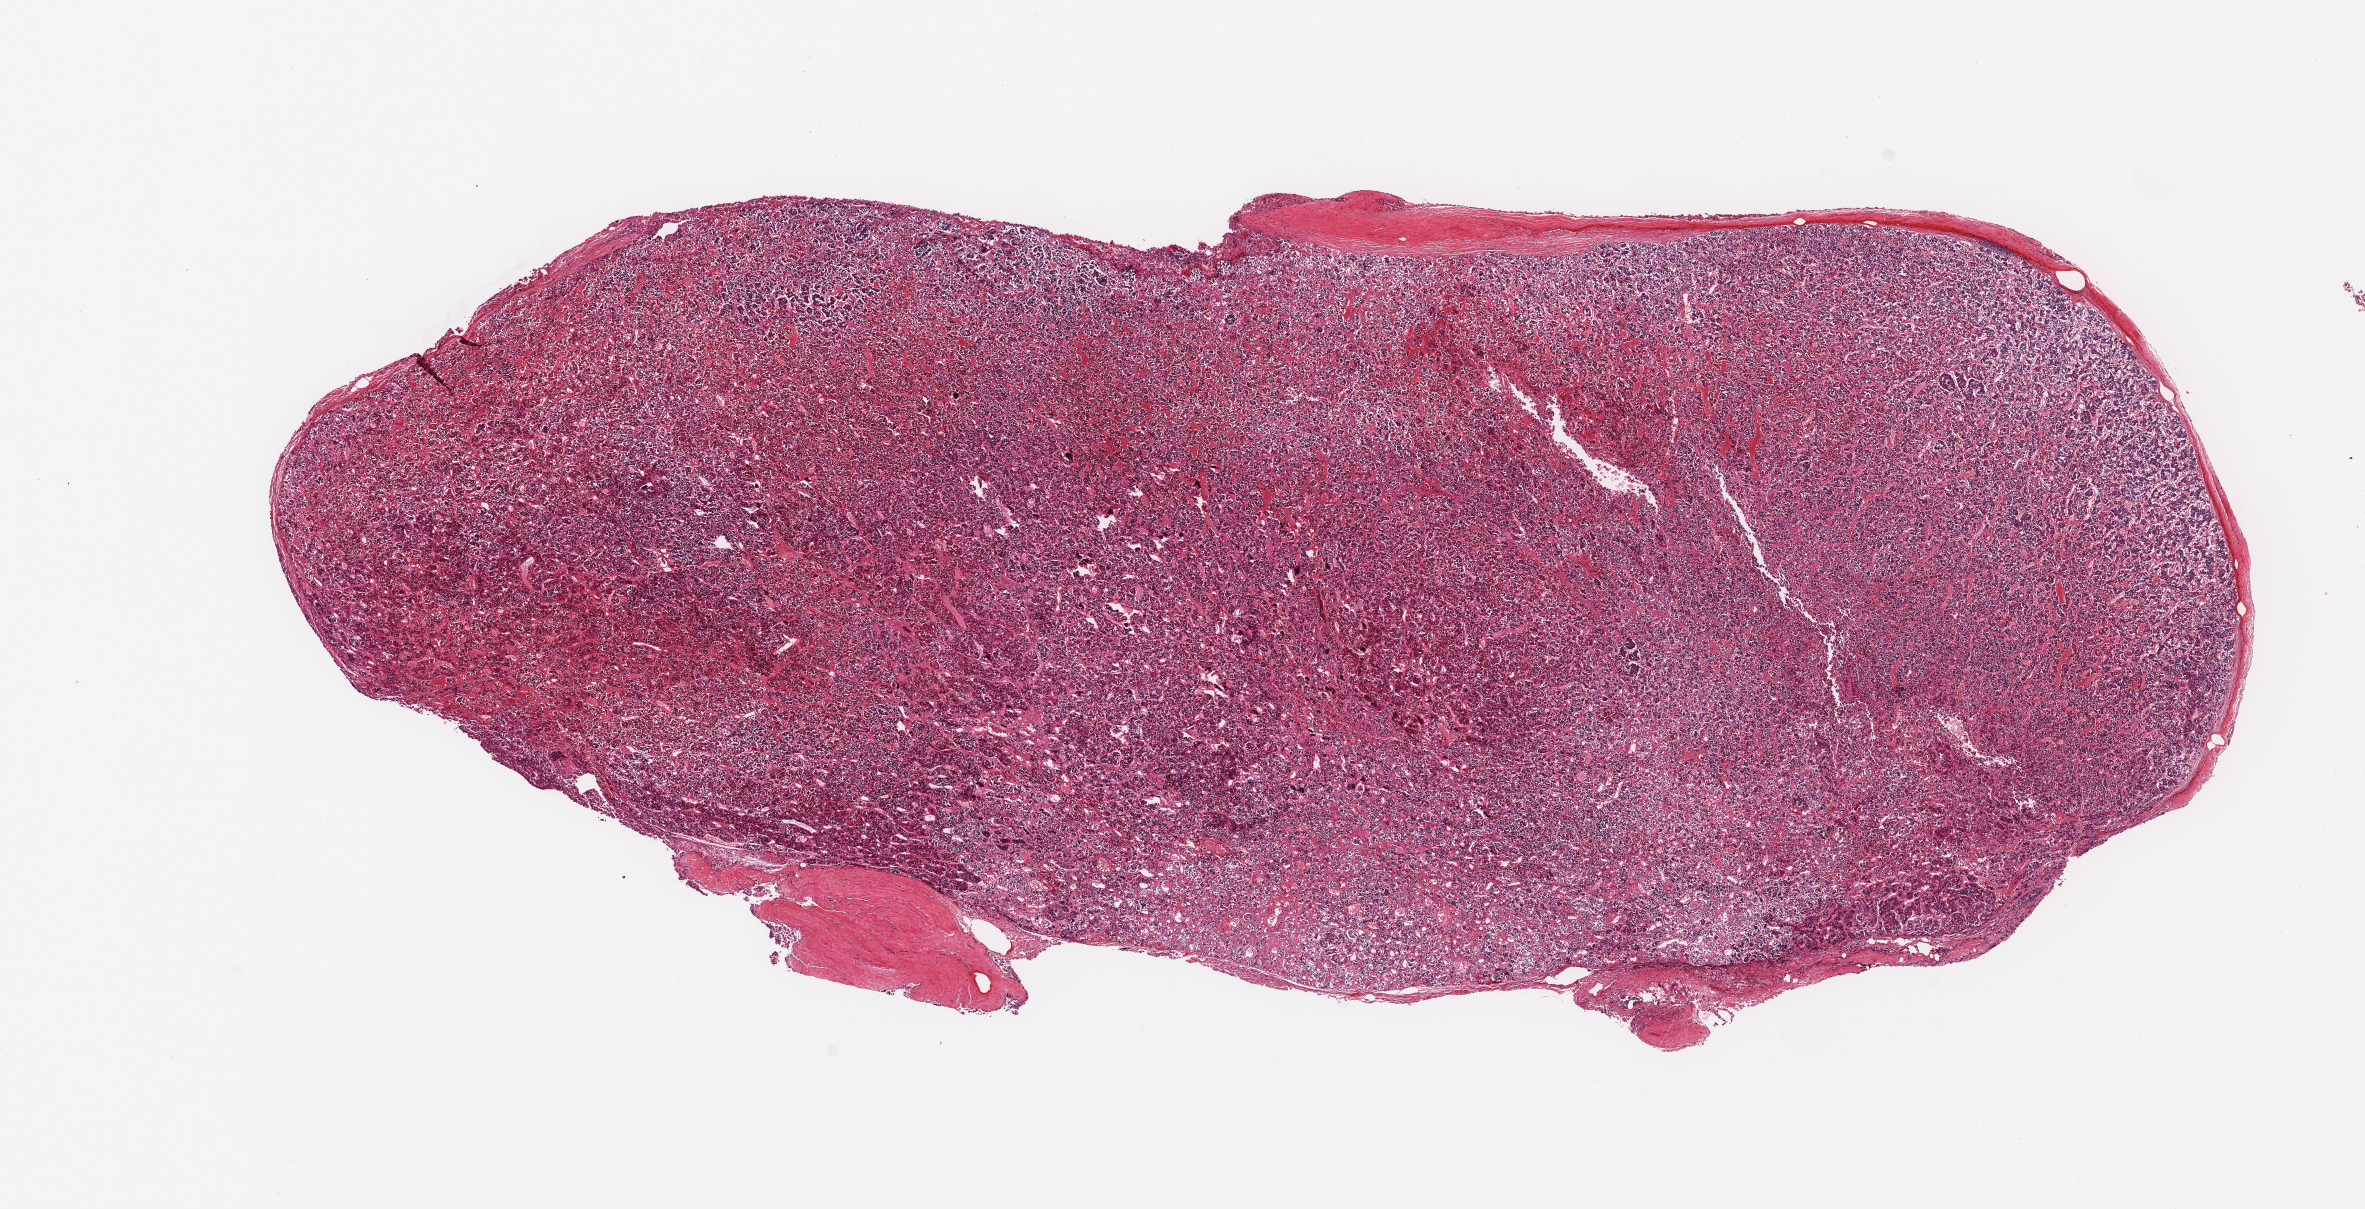
Digitized hematoxylin and eosin (H&E)-stained section — shown as a low-resolution overview of the whole scanned area (about 18.7 x 9.6 mm), PAXgene-fixed paraffin-embedded (PFPE) section, sampled site (target tissue): pituitary, tissue donor sample. Female donor.
Review note (as recorded): 1 piece; adenohypophysis.